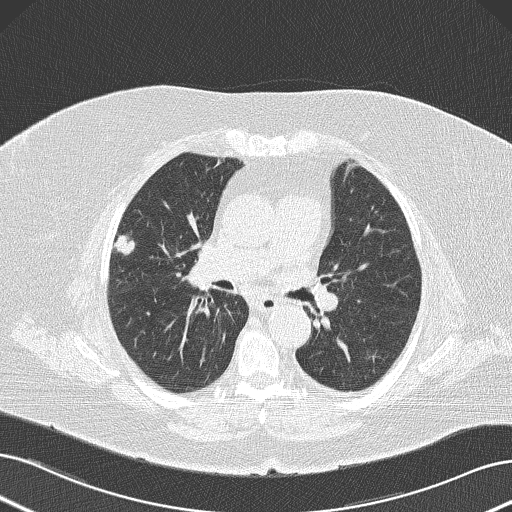
Axial slice from a low-dose chest CT screening exam, first (baseline) screen, lung window (W 1500 / L -600 HU), 2 mm slice thickness, slice 68 of 145 in the series, 512 × 512 image matrix, field of view 364 × 364 mm. Female participant, aged 73 years at enrolment. Former smoker at enrolment.
Expert-annotated lung lesion, bounding box (x1, y1, x2, y2) in pixels: (102, 220, 147, 262). Screening reader's record for this exam (one nodule recorded; not confirmed to be the boxed lesion): non-calcified nodule or mass ≥4 mm, right upper lobe, 15 × 11 mm, poorly defined margins, soft tissue attenuation. Official screen result: positive, change unspecified: nodule(s) >= 4 mm or enlarging nodule(s), mass(es), or other non-specific abnormalities suspicious for lung cancer. Lung cancer was diagnosed 55 days after this screen: neoplasm, malignant, right upper lobe, stage IA (AJCC 6th edition), 15 mm at pathology.